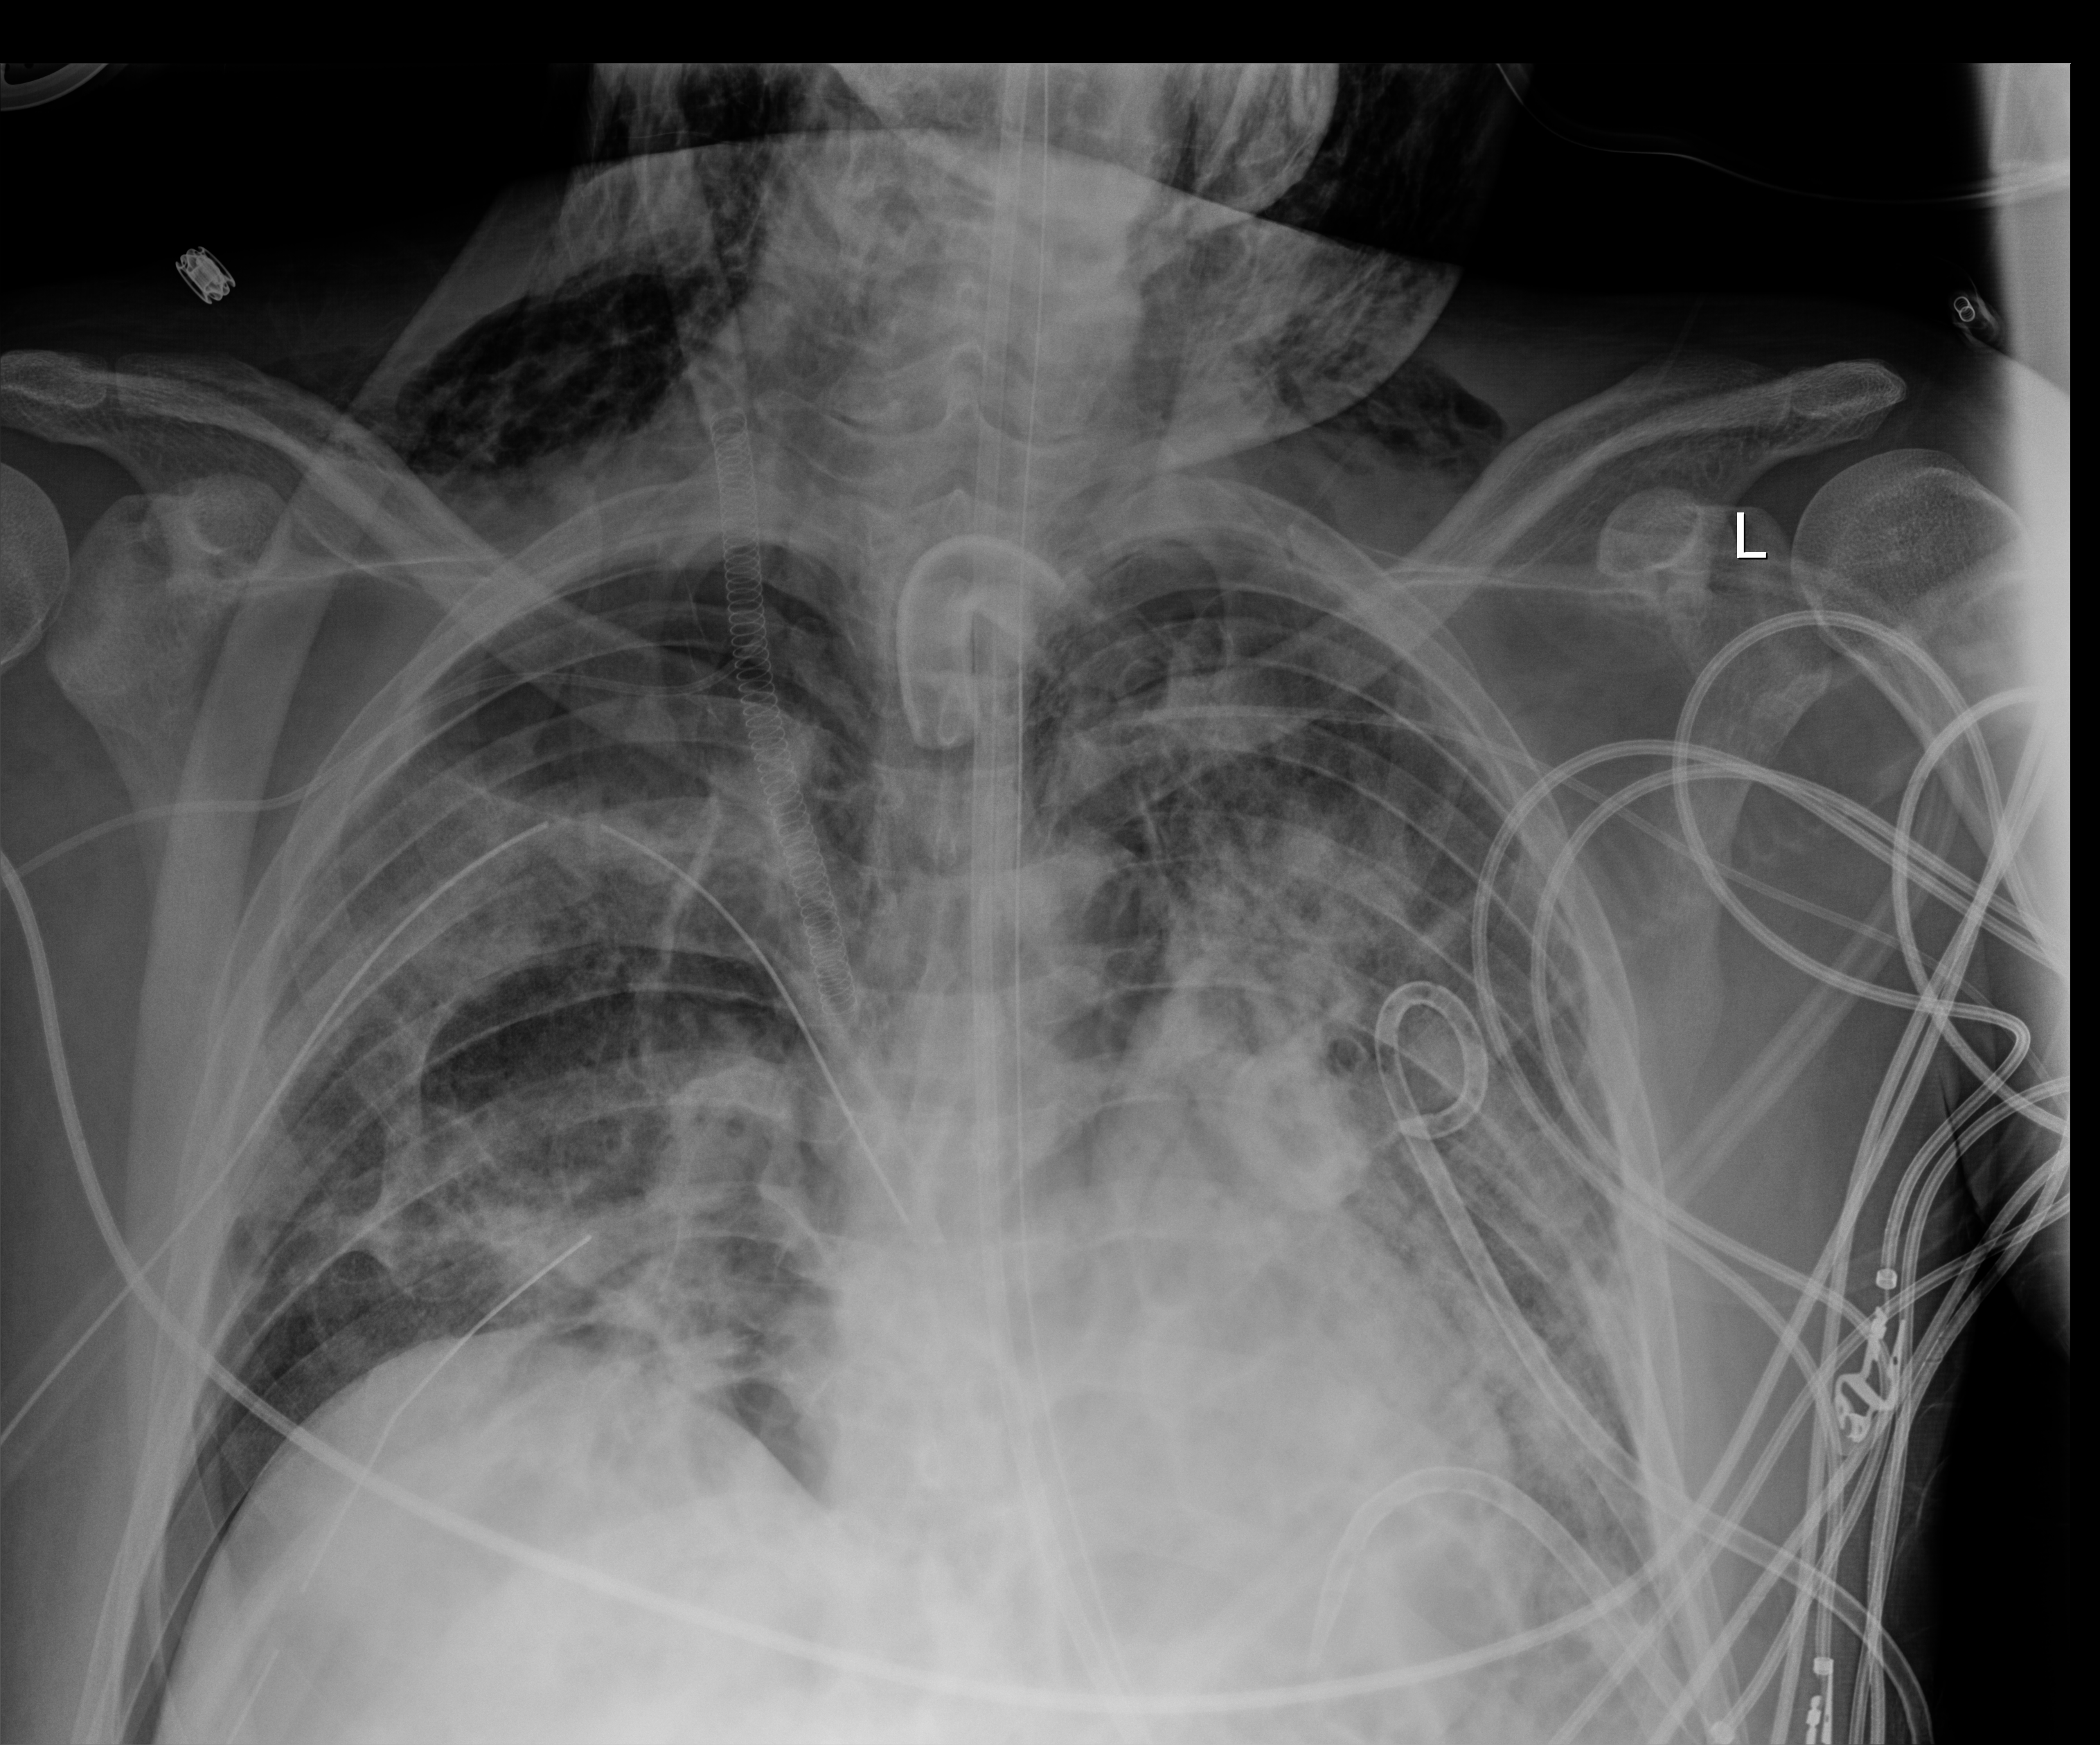
Chest X-ray, anteroposterior (AP) projection. Patient hospitalised with COVID-19, aged 18–59 years.
From the hospital-stay record, not from the radiograph (when in the stay this image was taken is not recorded): admitted to intensive care during this hospital stay: yes; chronic kidney disease (admission record): no; smoking status (admission record): never.